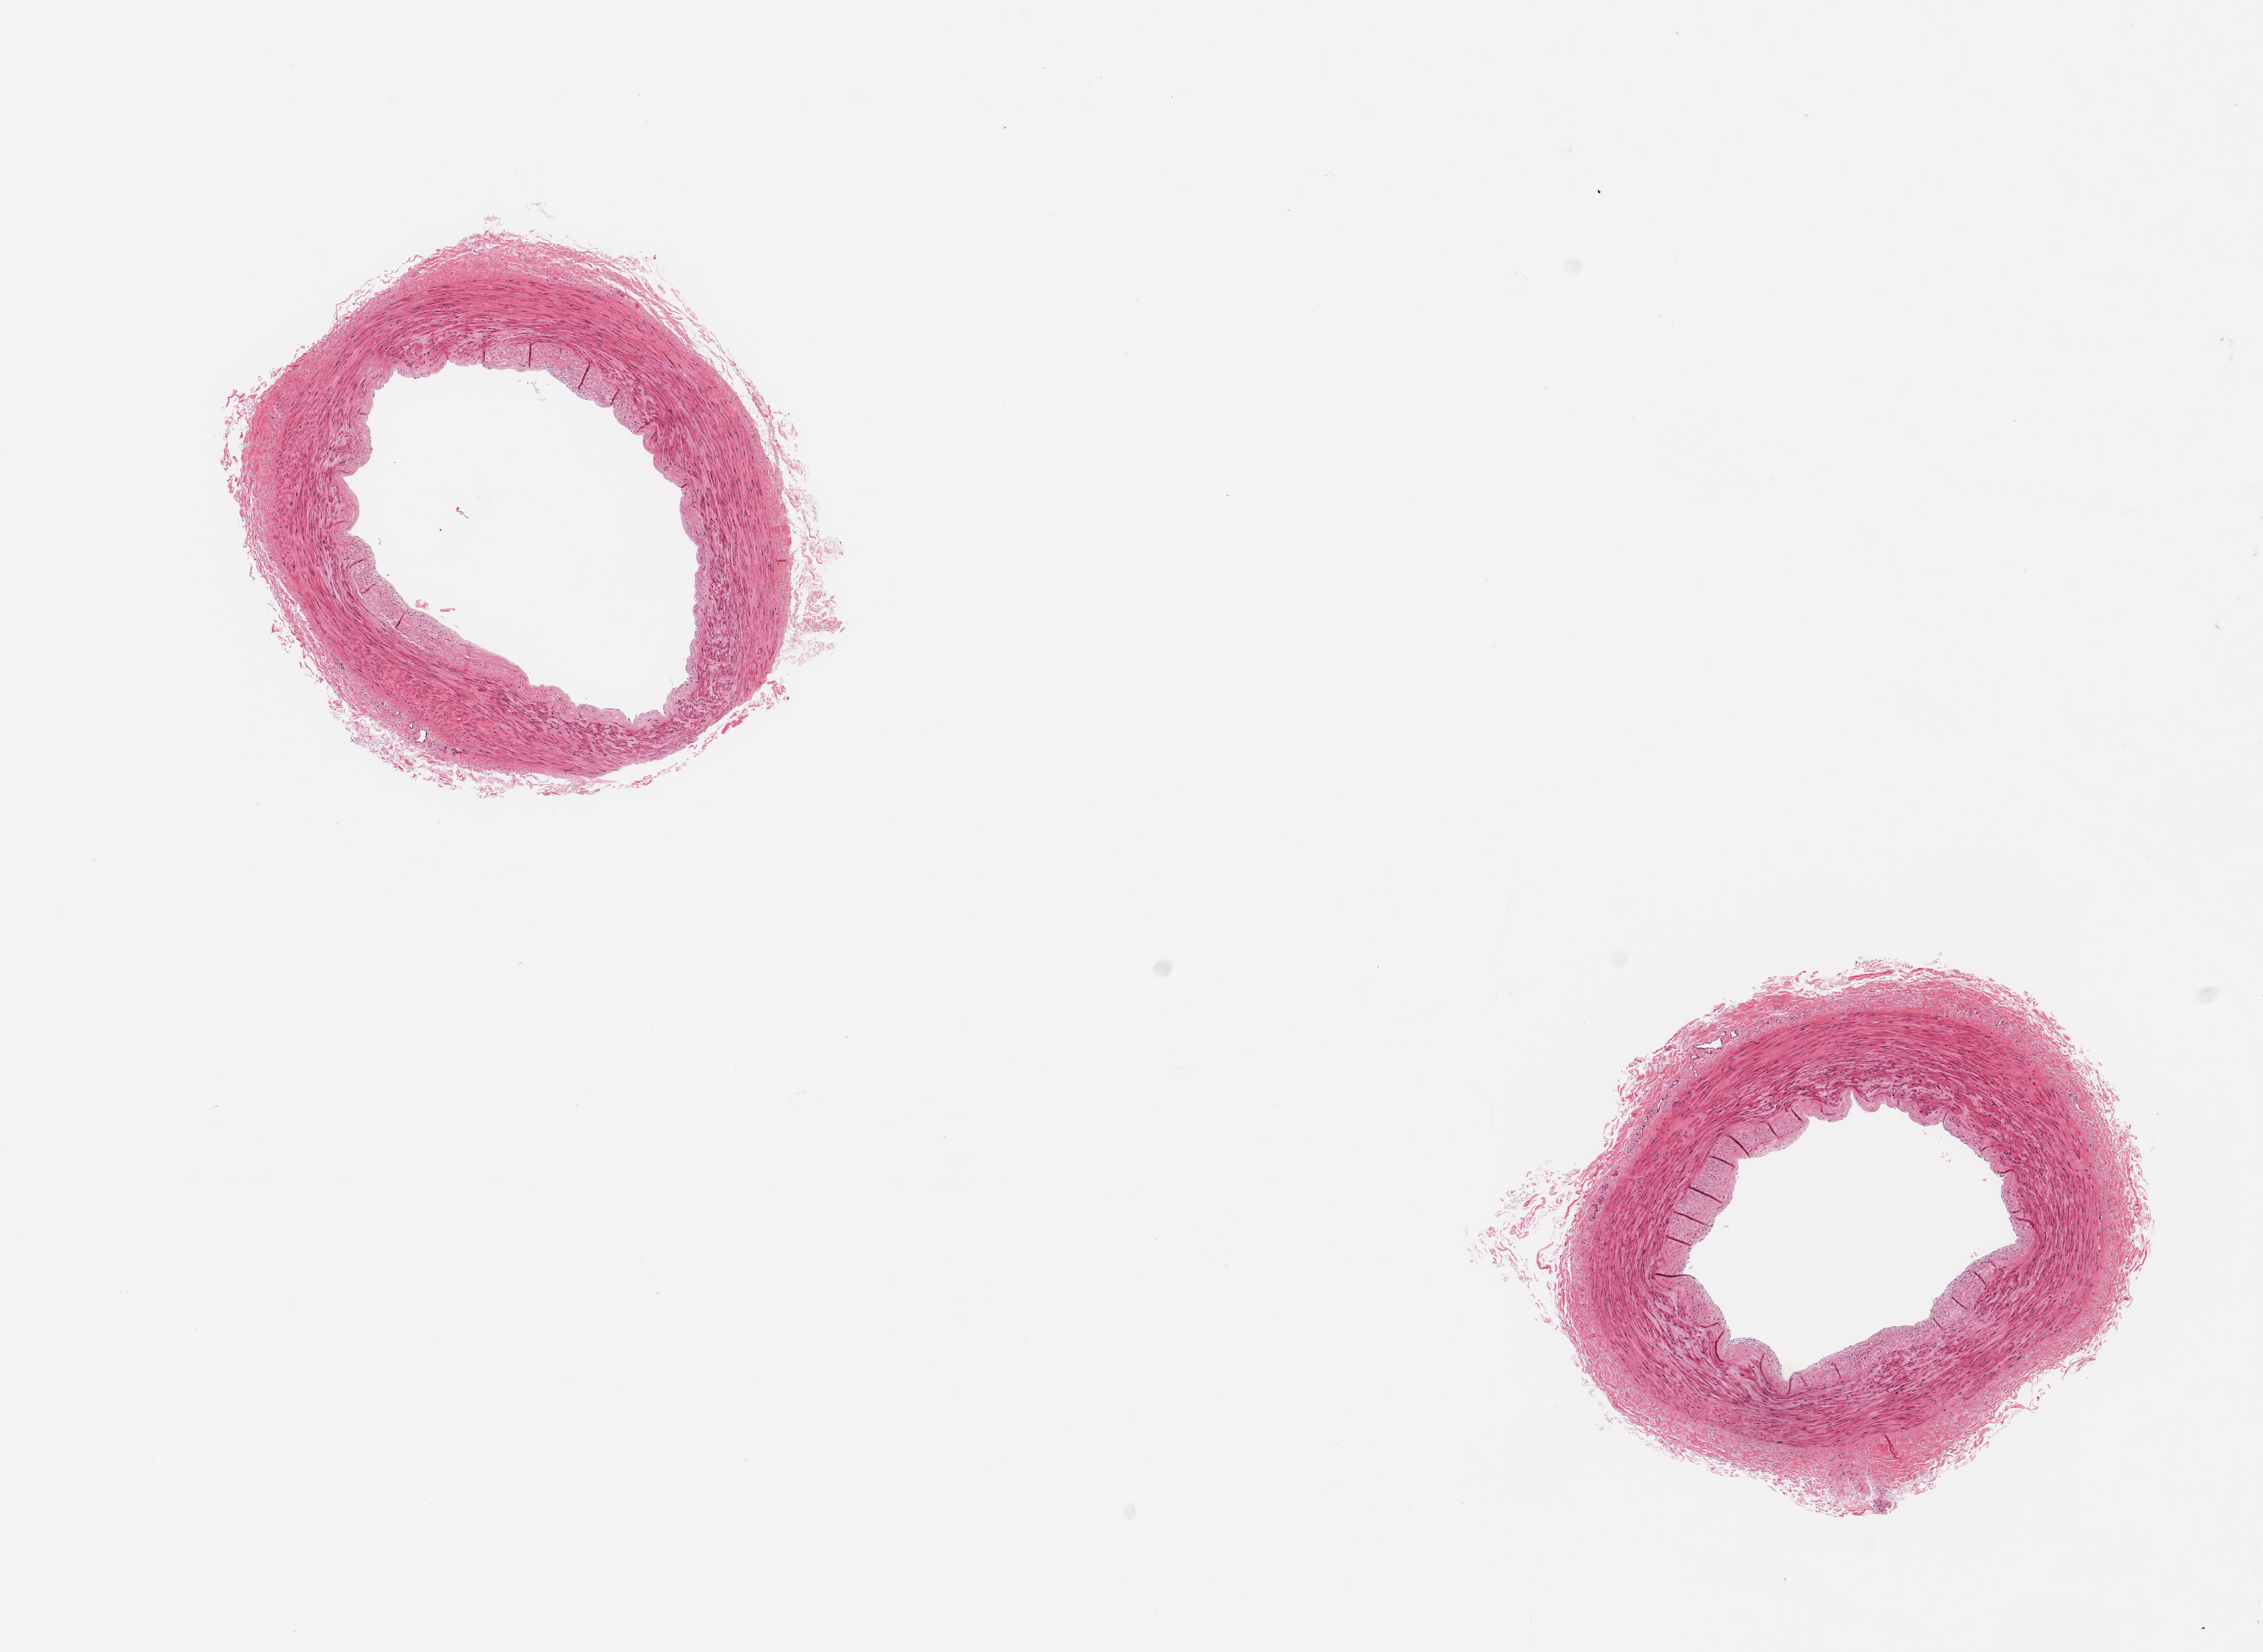
Whole-slide image, H&E stain — whole scanned area (about 11.8 x 8.6 mm) shown as a low-resolution overview; PAXgene-fixed, paraffin-embedded tissue; section of tibial artery (target tissue); donor tissue sample. Donor sex: male.
* pathologist's review note for this sample: 2 pieces; well trimmed